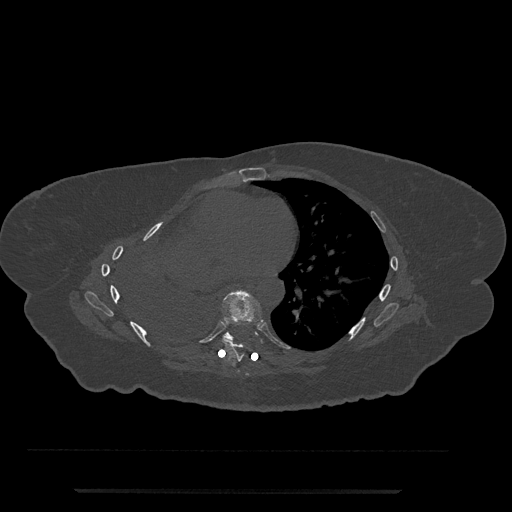
CT including the spine, one axial slice. Position 426 of 797 along the scan axis. Bone window (W 1800 / L 400 HU). 512 × 512 image matrix, field of view 440 × 440 mm. Female patient, age 51 years. Case-level facts recorded for this patient, not image findings: primary cancer: neuro; vertebrae with lytic lesions (as recorded): T8.
Structures marked on this image (semi-automatically segmented with operator editing):
- T7 vertebra: bounding box <222,290,263,362> (left, top, right, bottom; pixels)
- T8 vertebra: <223,330,234,341>